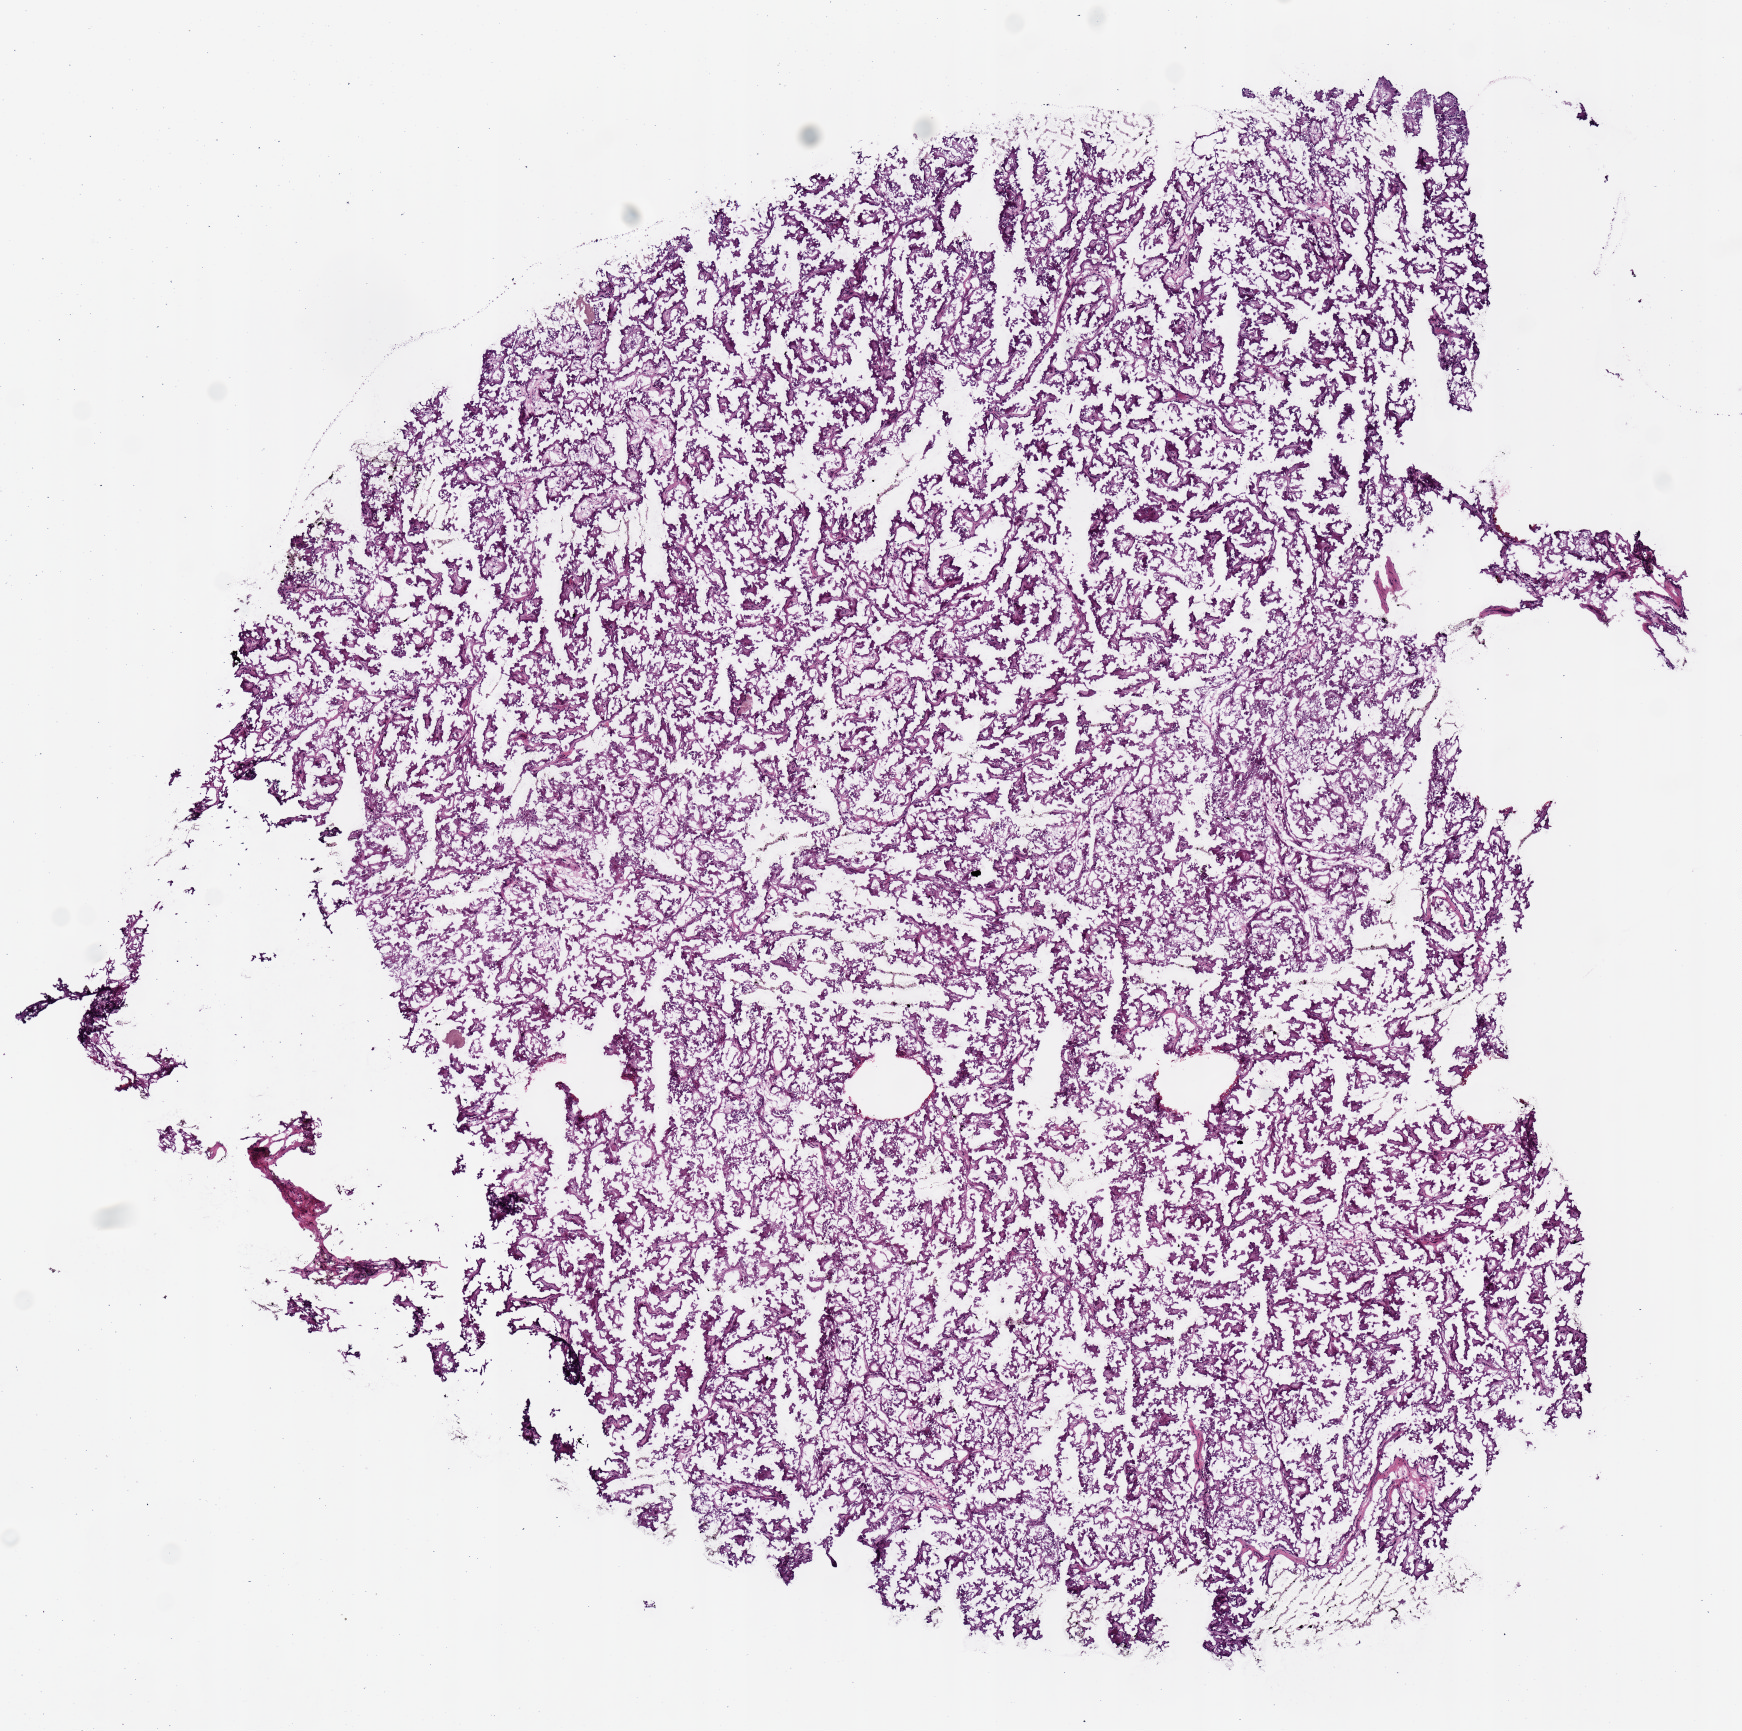
Digitized Hematoxylin and eosin (H&E) stained tissue section (whole slide), shown as a low-resolution overview of the whole scanned area (about 6.9 x 6.8 mm, acquisition: 20x scan), frozen section from the top of the tissue portion, primary tumour sample from the kidney. Male patient; age at initial diagnosis 60 years.
Diagnosis: Papillary adenocarcinoma, NOS.